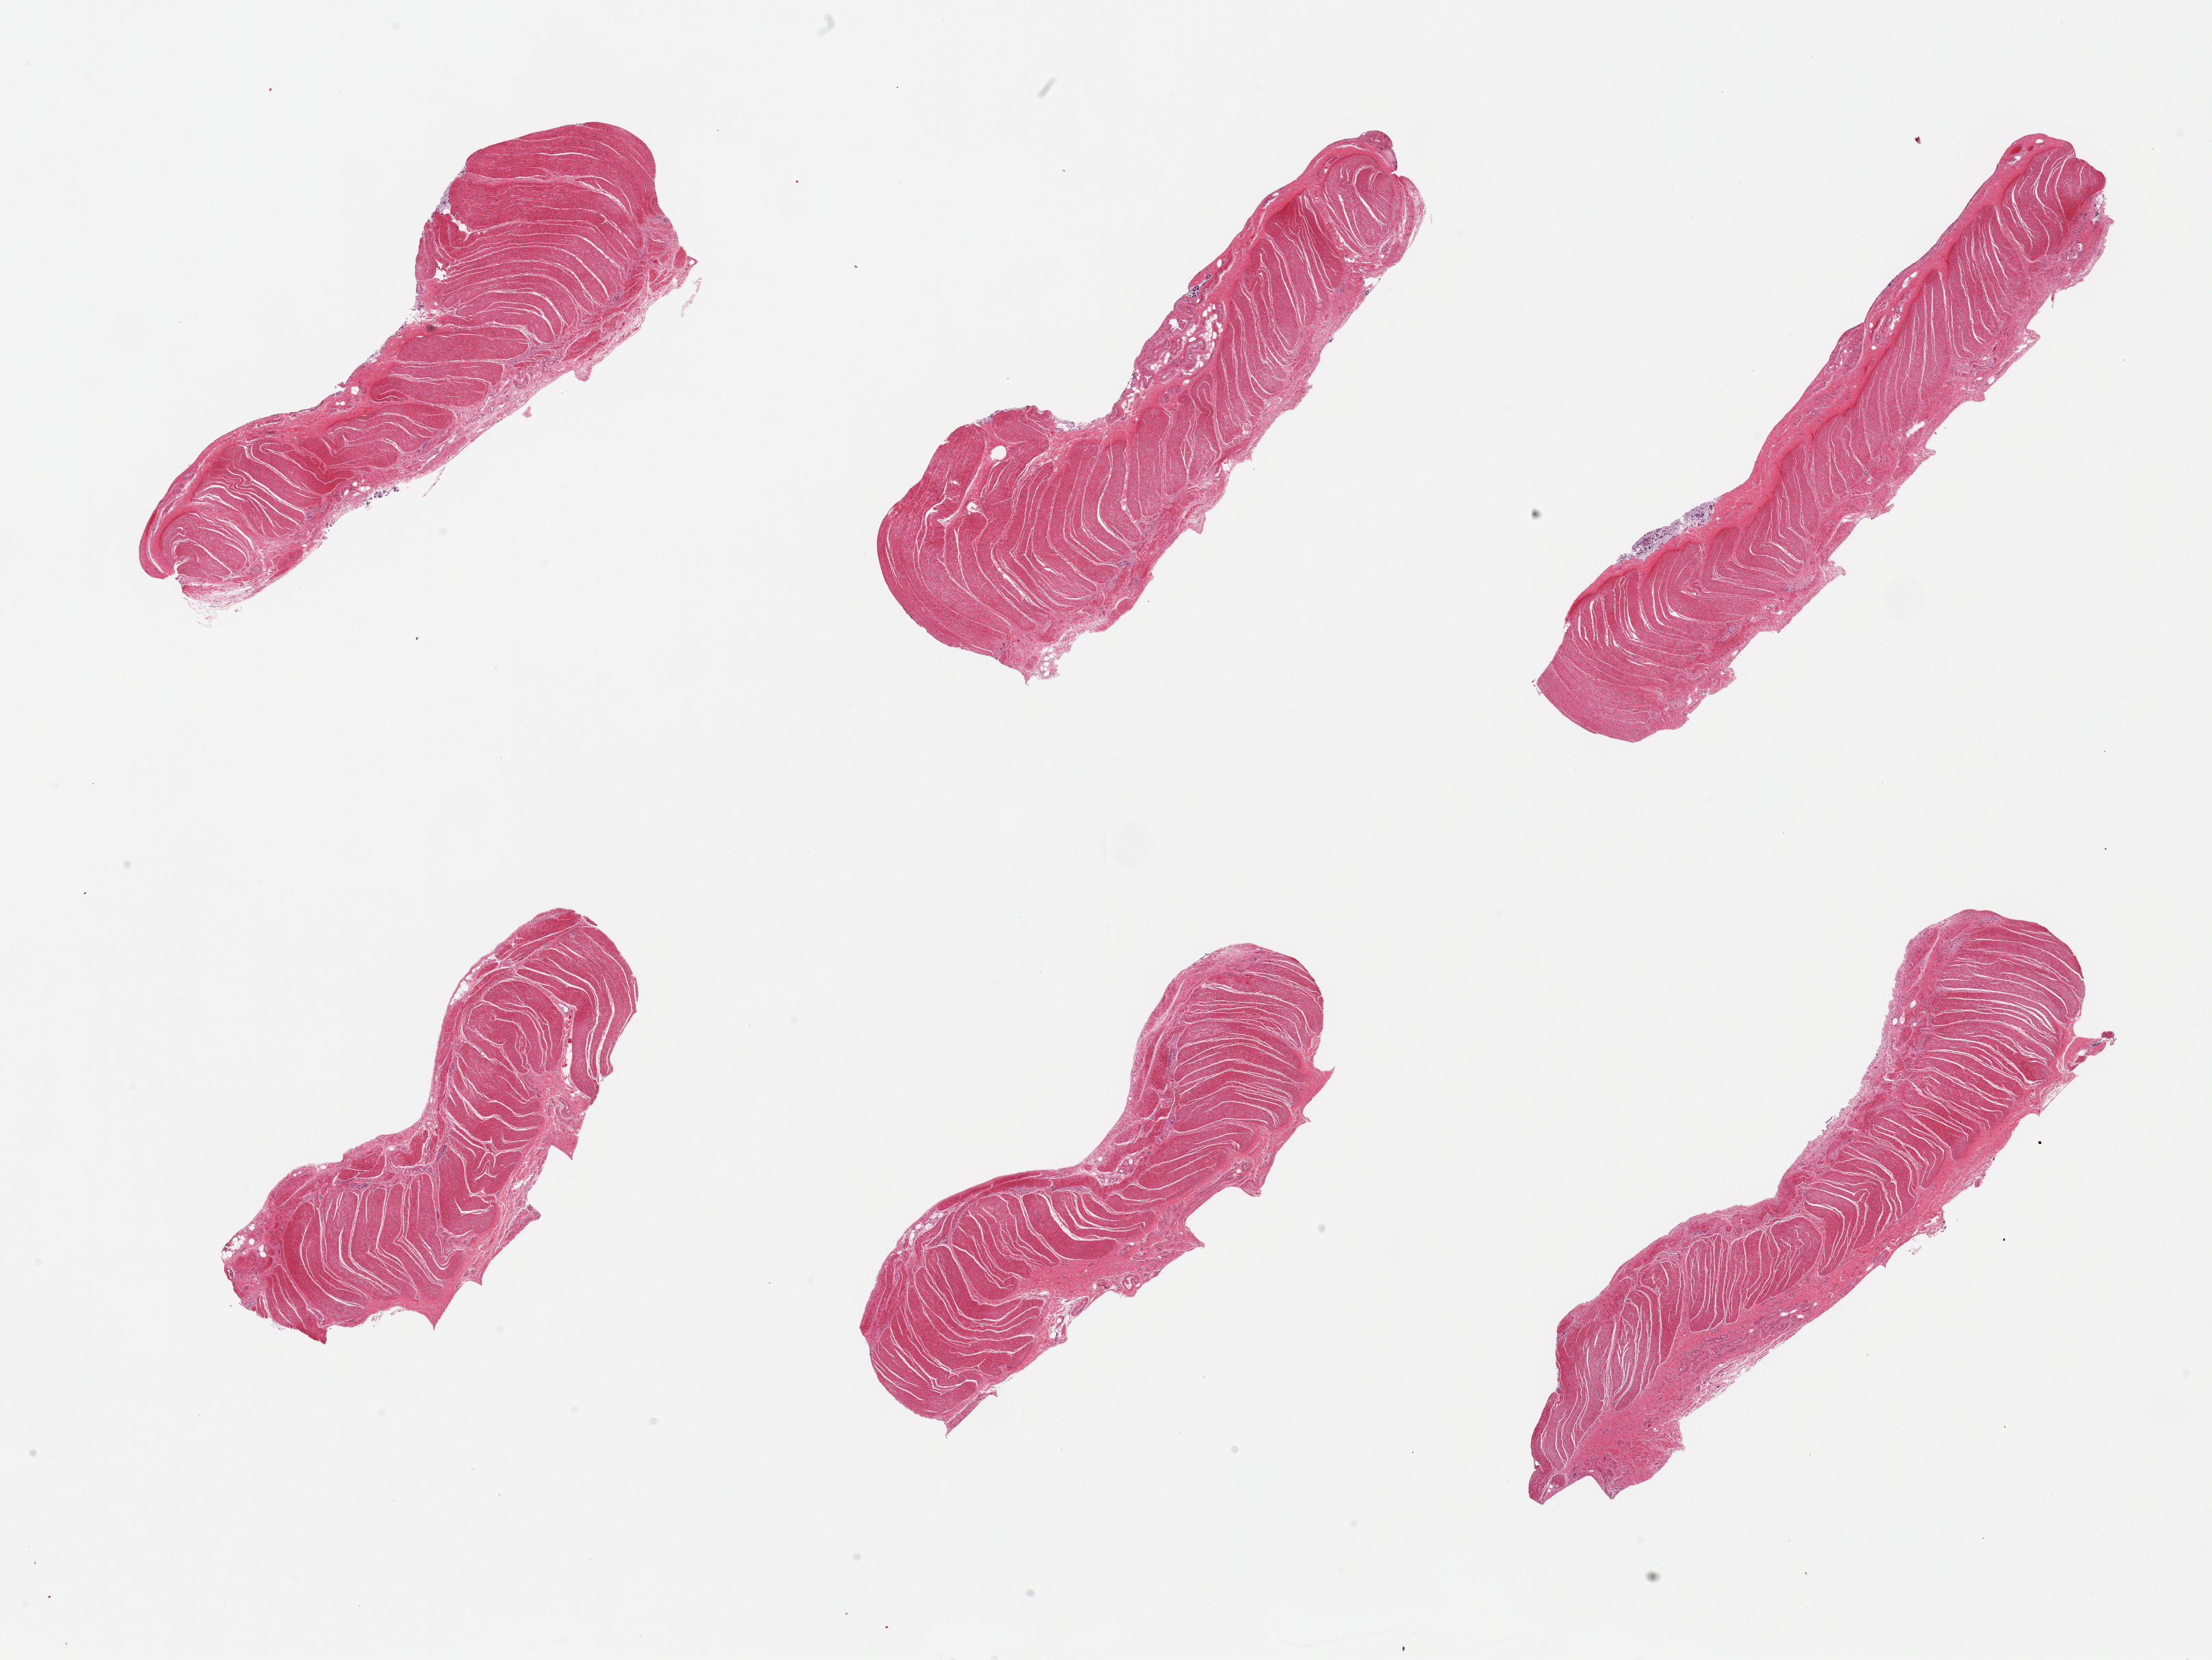
Digitized hematoxylin and eosin (H&E)-stained section, a low-resolution overview of the entire scanned area, about 25.6 x 19.2 mm. PAXgene-fixed paraffin-embedded (PFPE) section. Target tissue: sigmoid colon. Tissue donor sample. Donor: male.
Reviewer comment on this tissue sample: 6 pieces, target muscularis.